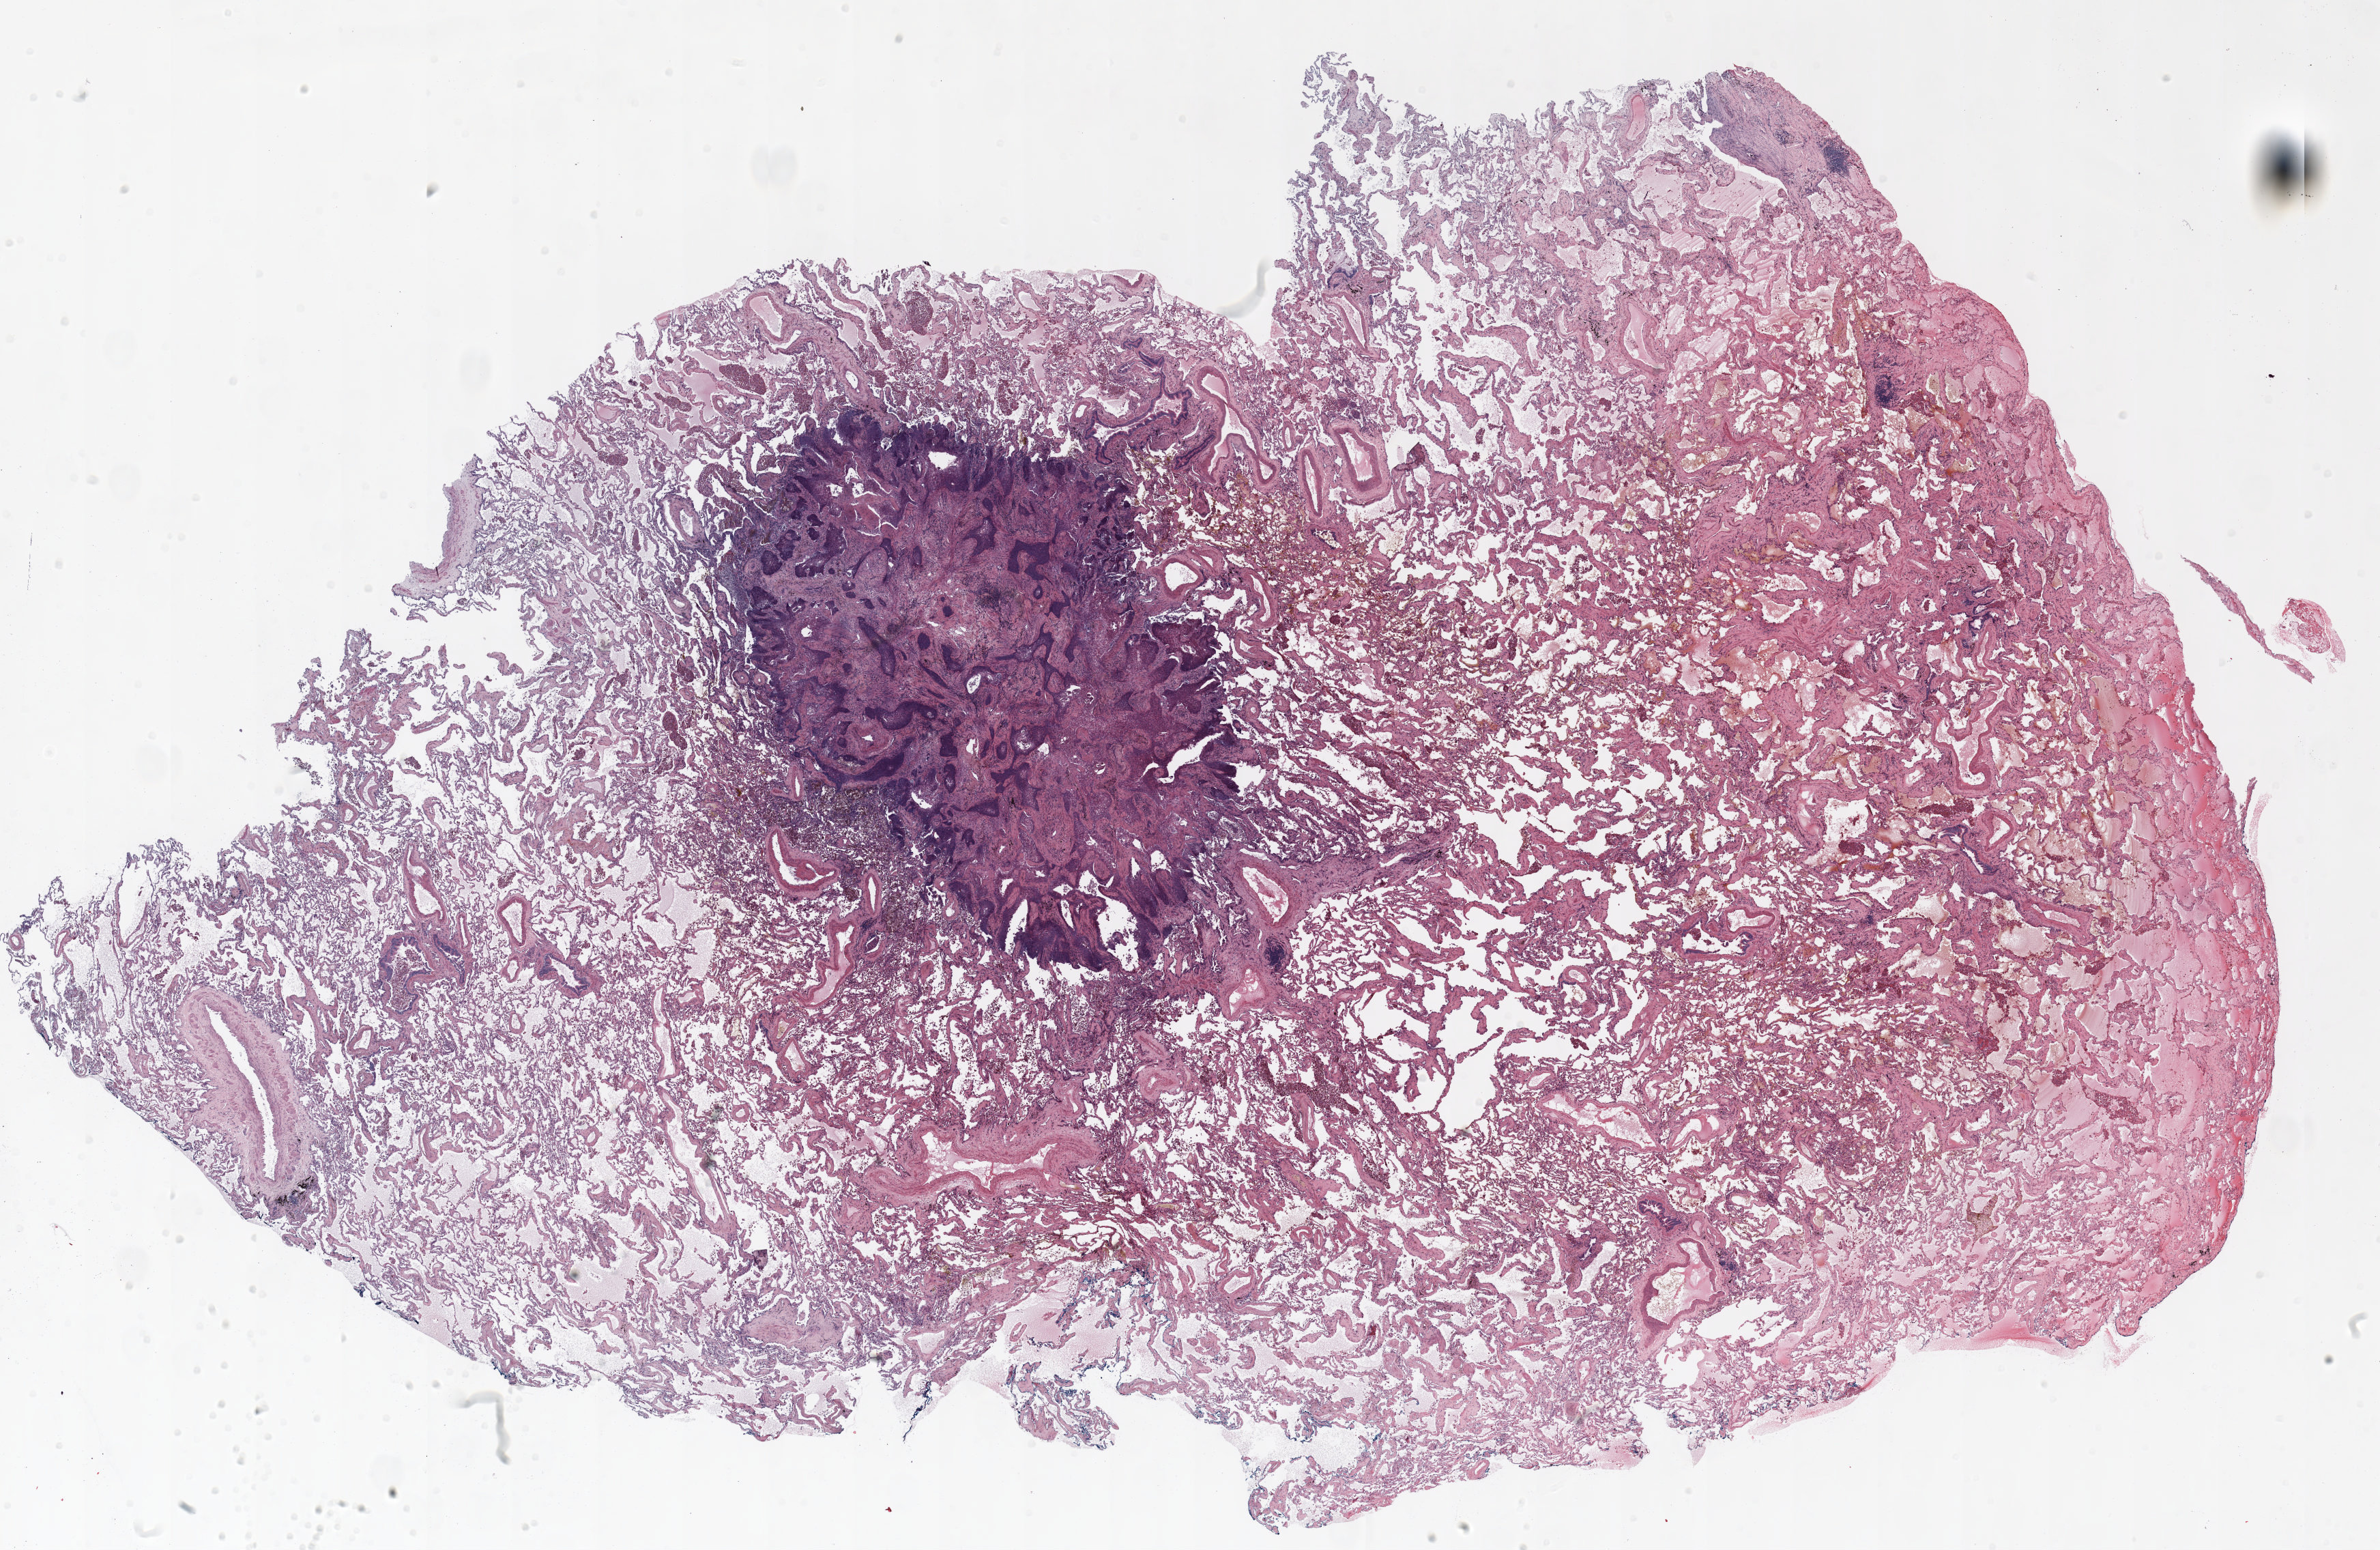
Whole-slide histology image, H&E-stained, a low-resolution overview of the entire scanned area, about 28.0 x 18.2 mm (slide scanned at 20x). Formalin-fixed paraffin-embedded (FFPE) section. Lung tissue. Female, age 60 at enrolment.
Participant's lung-cancer diagnosis: Squamous cell carcinoma, keratinizing, NOS. Note: participant had 2 primary lung cancers recorded; fields above describe the first.